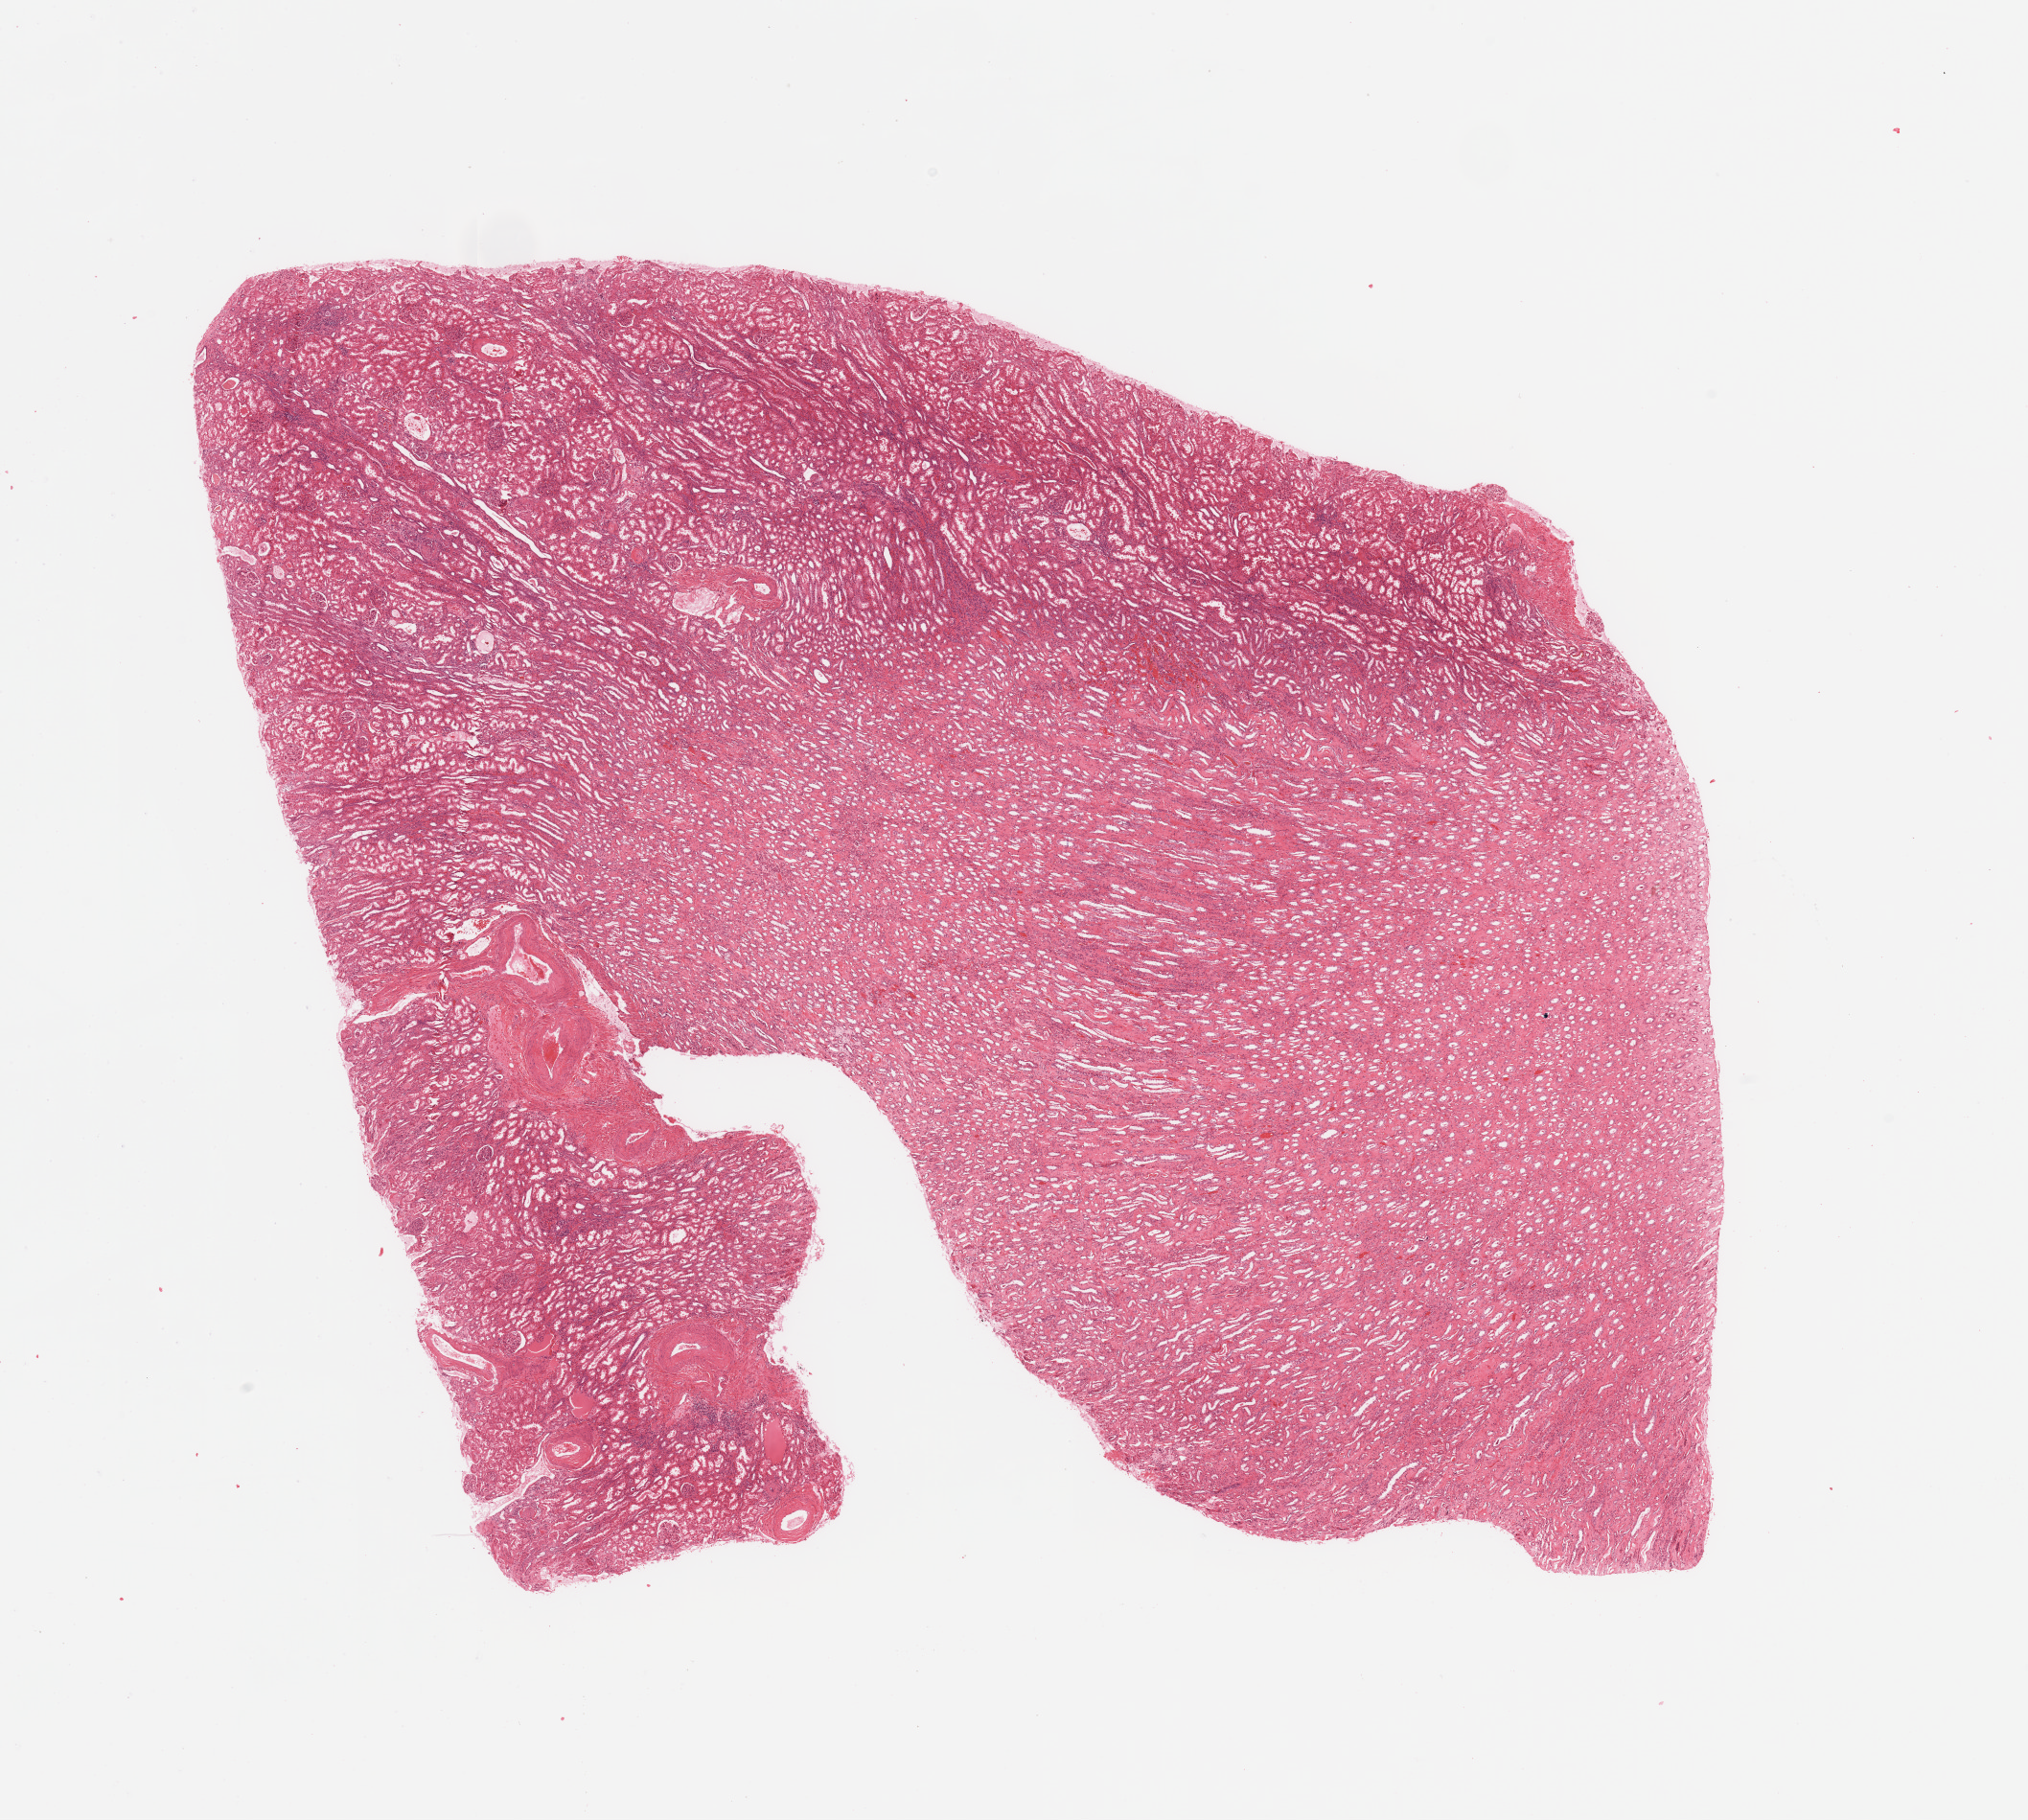
Digitized Hematoxylin and eosin (H&E) stained tissue section (whole slide), shown as a low-resolution overview of the whole scanned area (about 16.7 x 15.0 mm); normal (non-tumour) tissue sample, sampled site: kidney. Patient: male, age 72 years.
This section: normal (non-tumour) tissue from the same patient. Patient diagnosis: Renal cell carcinoma, NOS.